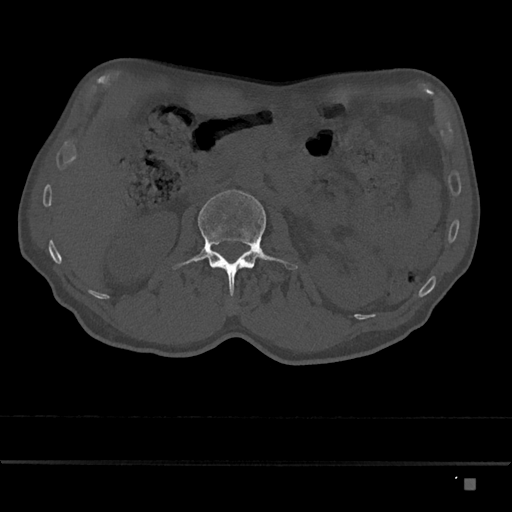
CT including the spine, one axial slice; position 477 of 797 along the scan axis; reconstruction kernel Br40s/3; bone window (W 1800 / L 400 HU); 0.5 mm slice thickness; 512 × 512 image matrix, field of view 390 × 390 mm. Patient: male, 72 years. Case-level facts recorded for this patient, not image findings: primary cancer: prostate.
Structures marked on this image (semi-automatically segmented with operator editing):
- L2 vertebra: box from (x=173, y=190) to (x=298, y=296) px